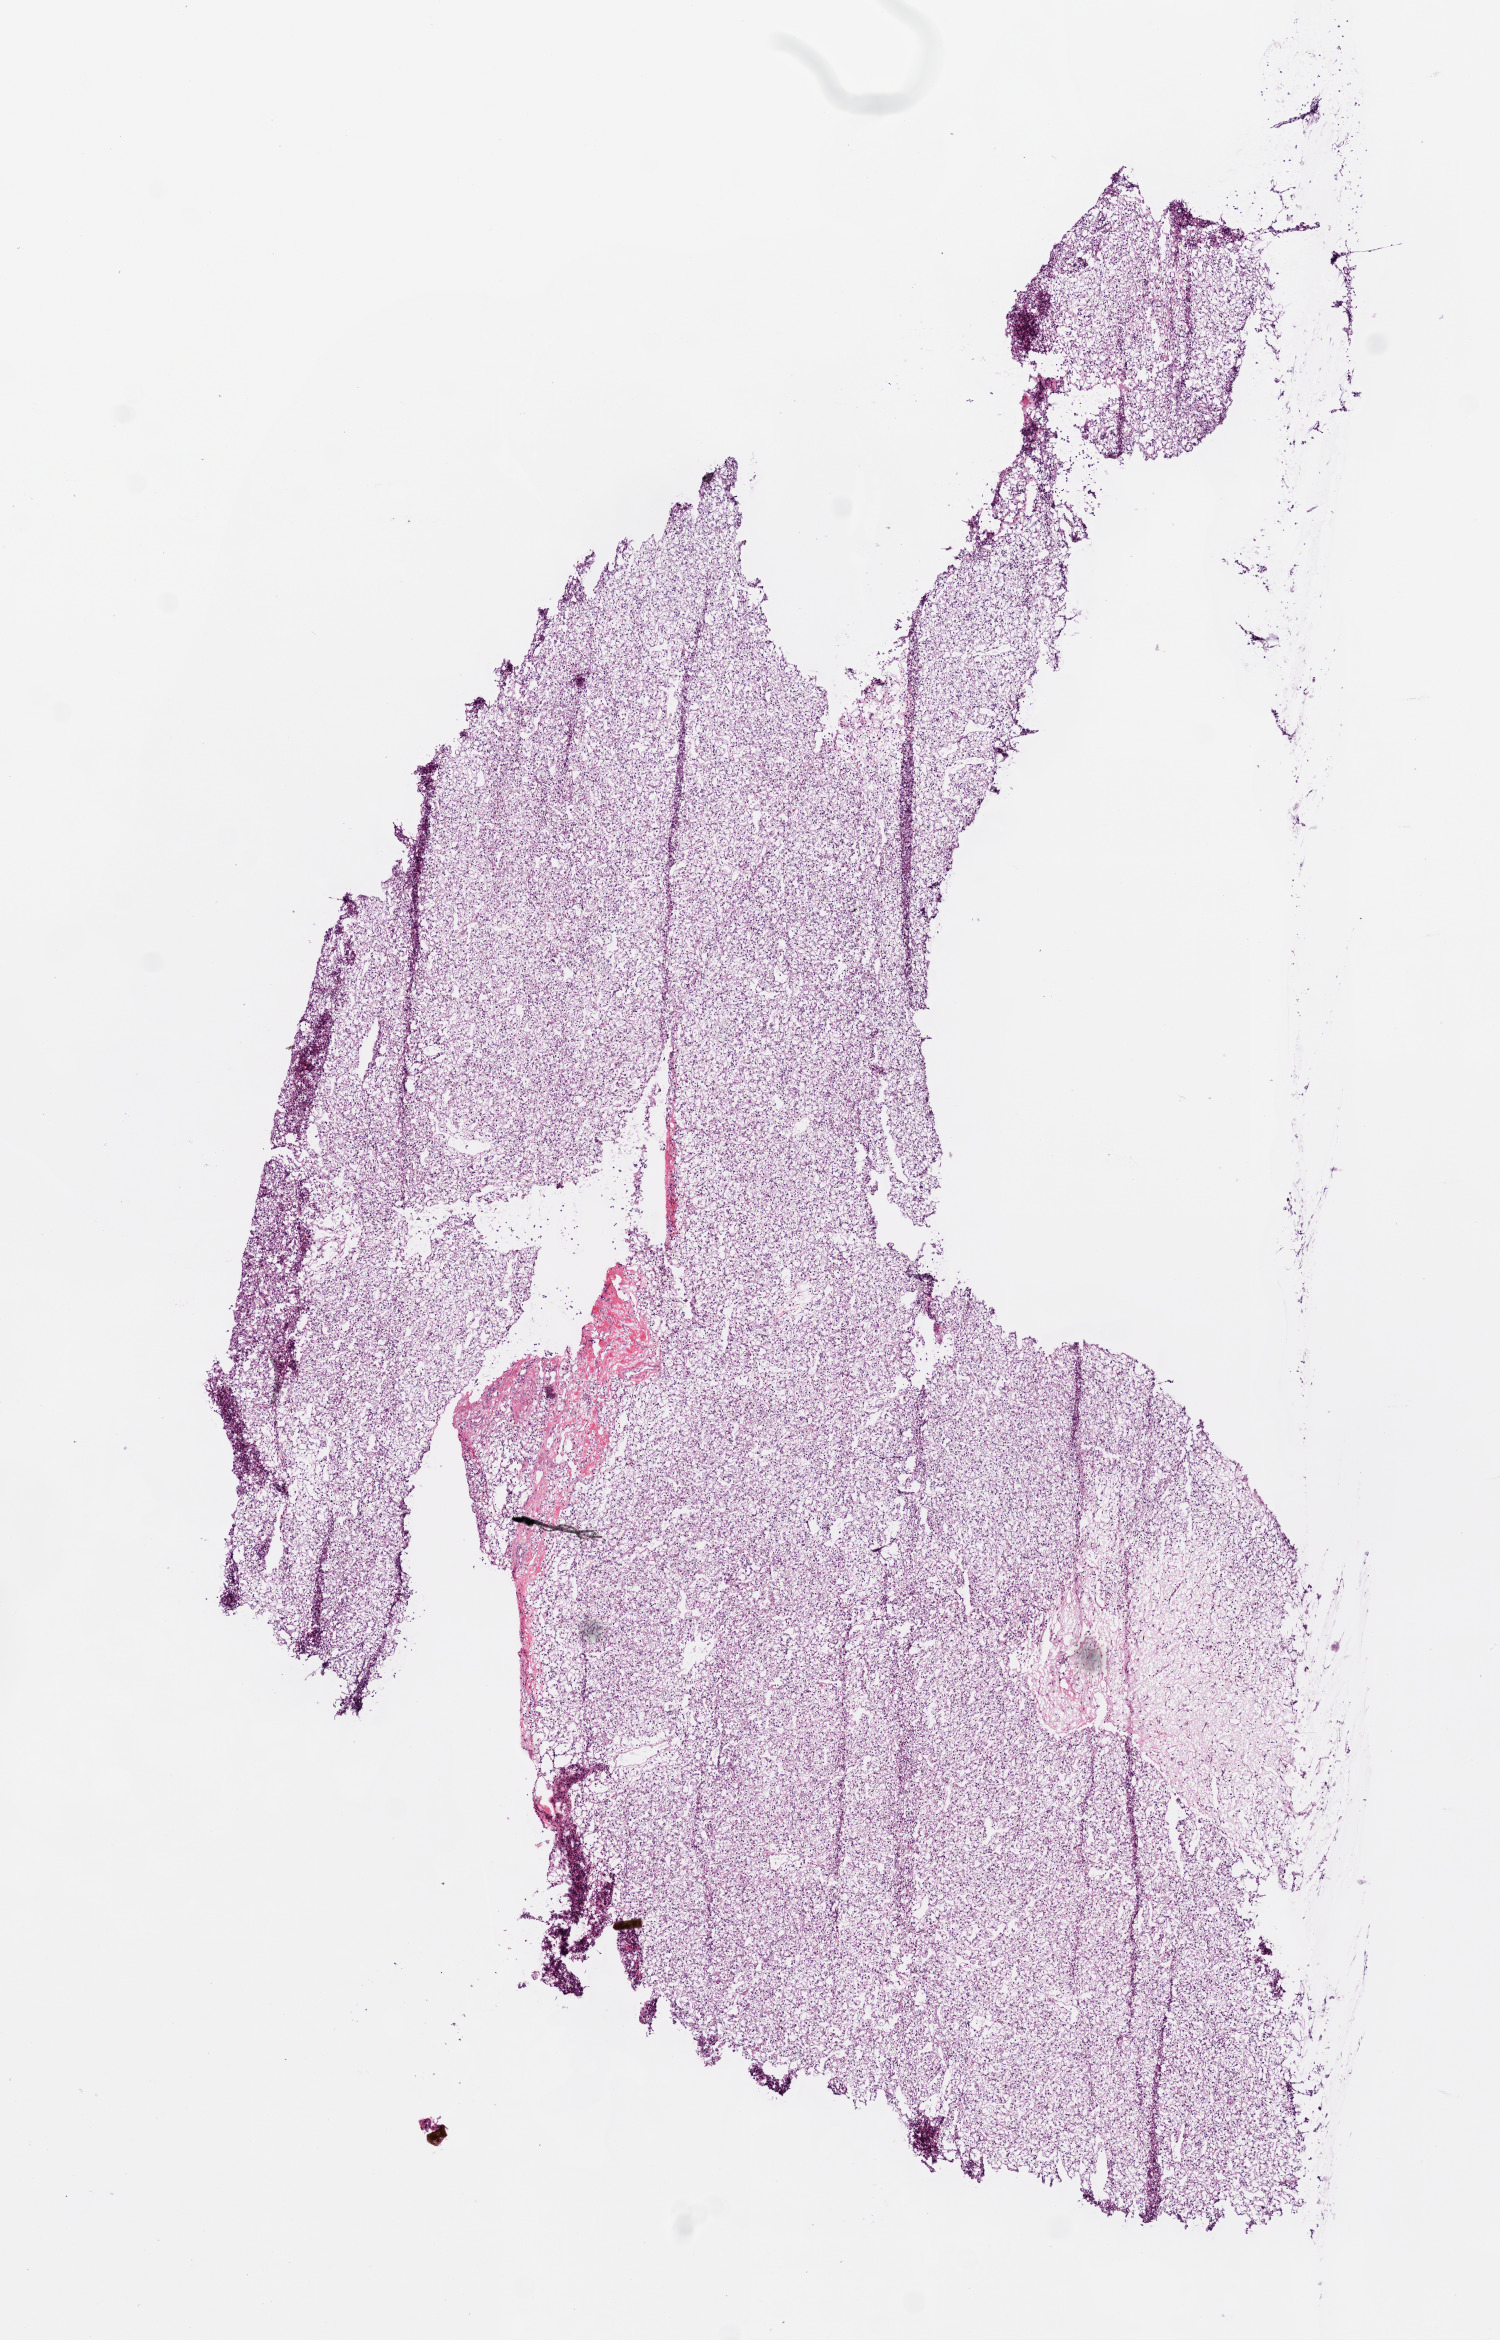
H&E whole-slide image, a low-resolution overview of the entire scanned area, about 6.0 x 9.4 mm (slide scanned at 20x). Frozen section from the top of the tissue portion. Sample: primary tumour, kidney. Female patient; age at initial diagnosis 73 years. Histologic grade: G2 (moderately differentiated). Composition of this section per pathologist review: tumour cells 80%, tumour nuclei 90%, normal cells 0%, stromal cells 10%, necrosis 10%.
• diagnosis: Clear cell adenocarcinoma, NOS
• laterality: left
• AJCC pathologic stage: I (7th edition)